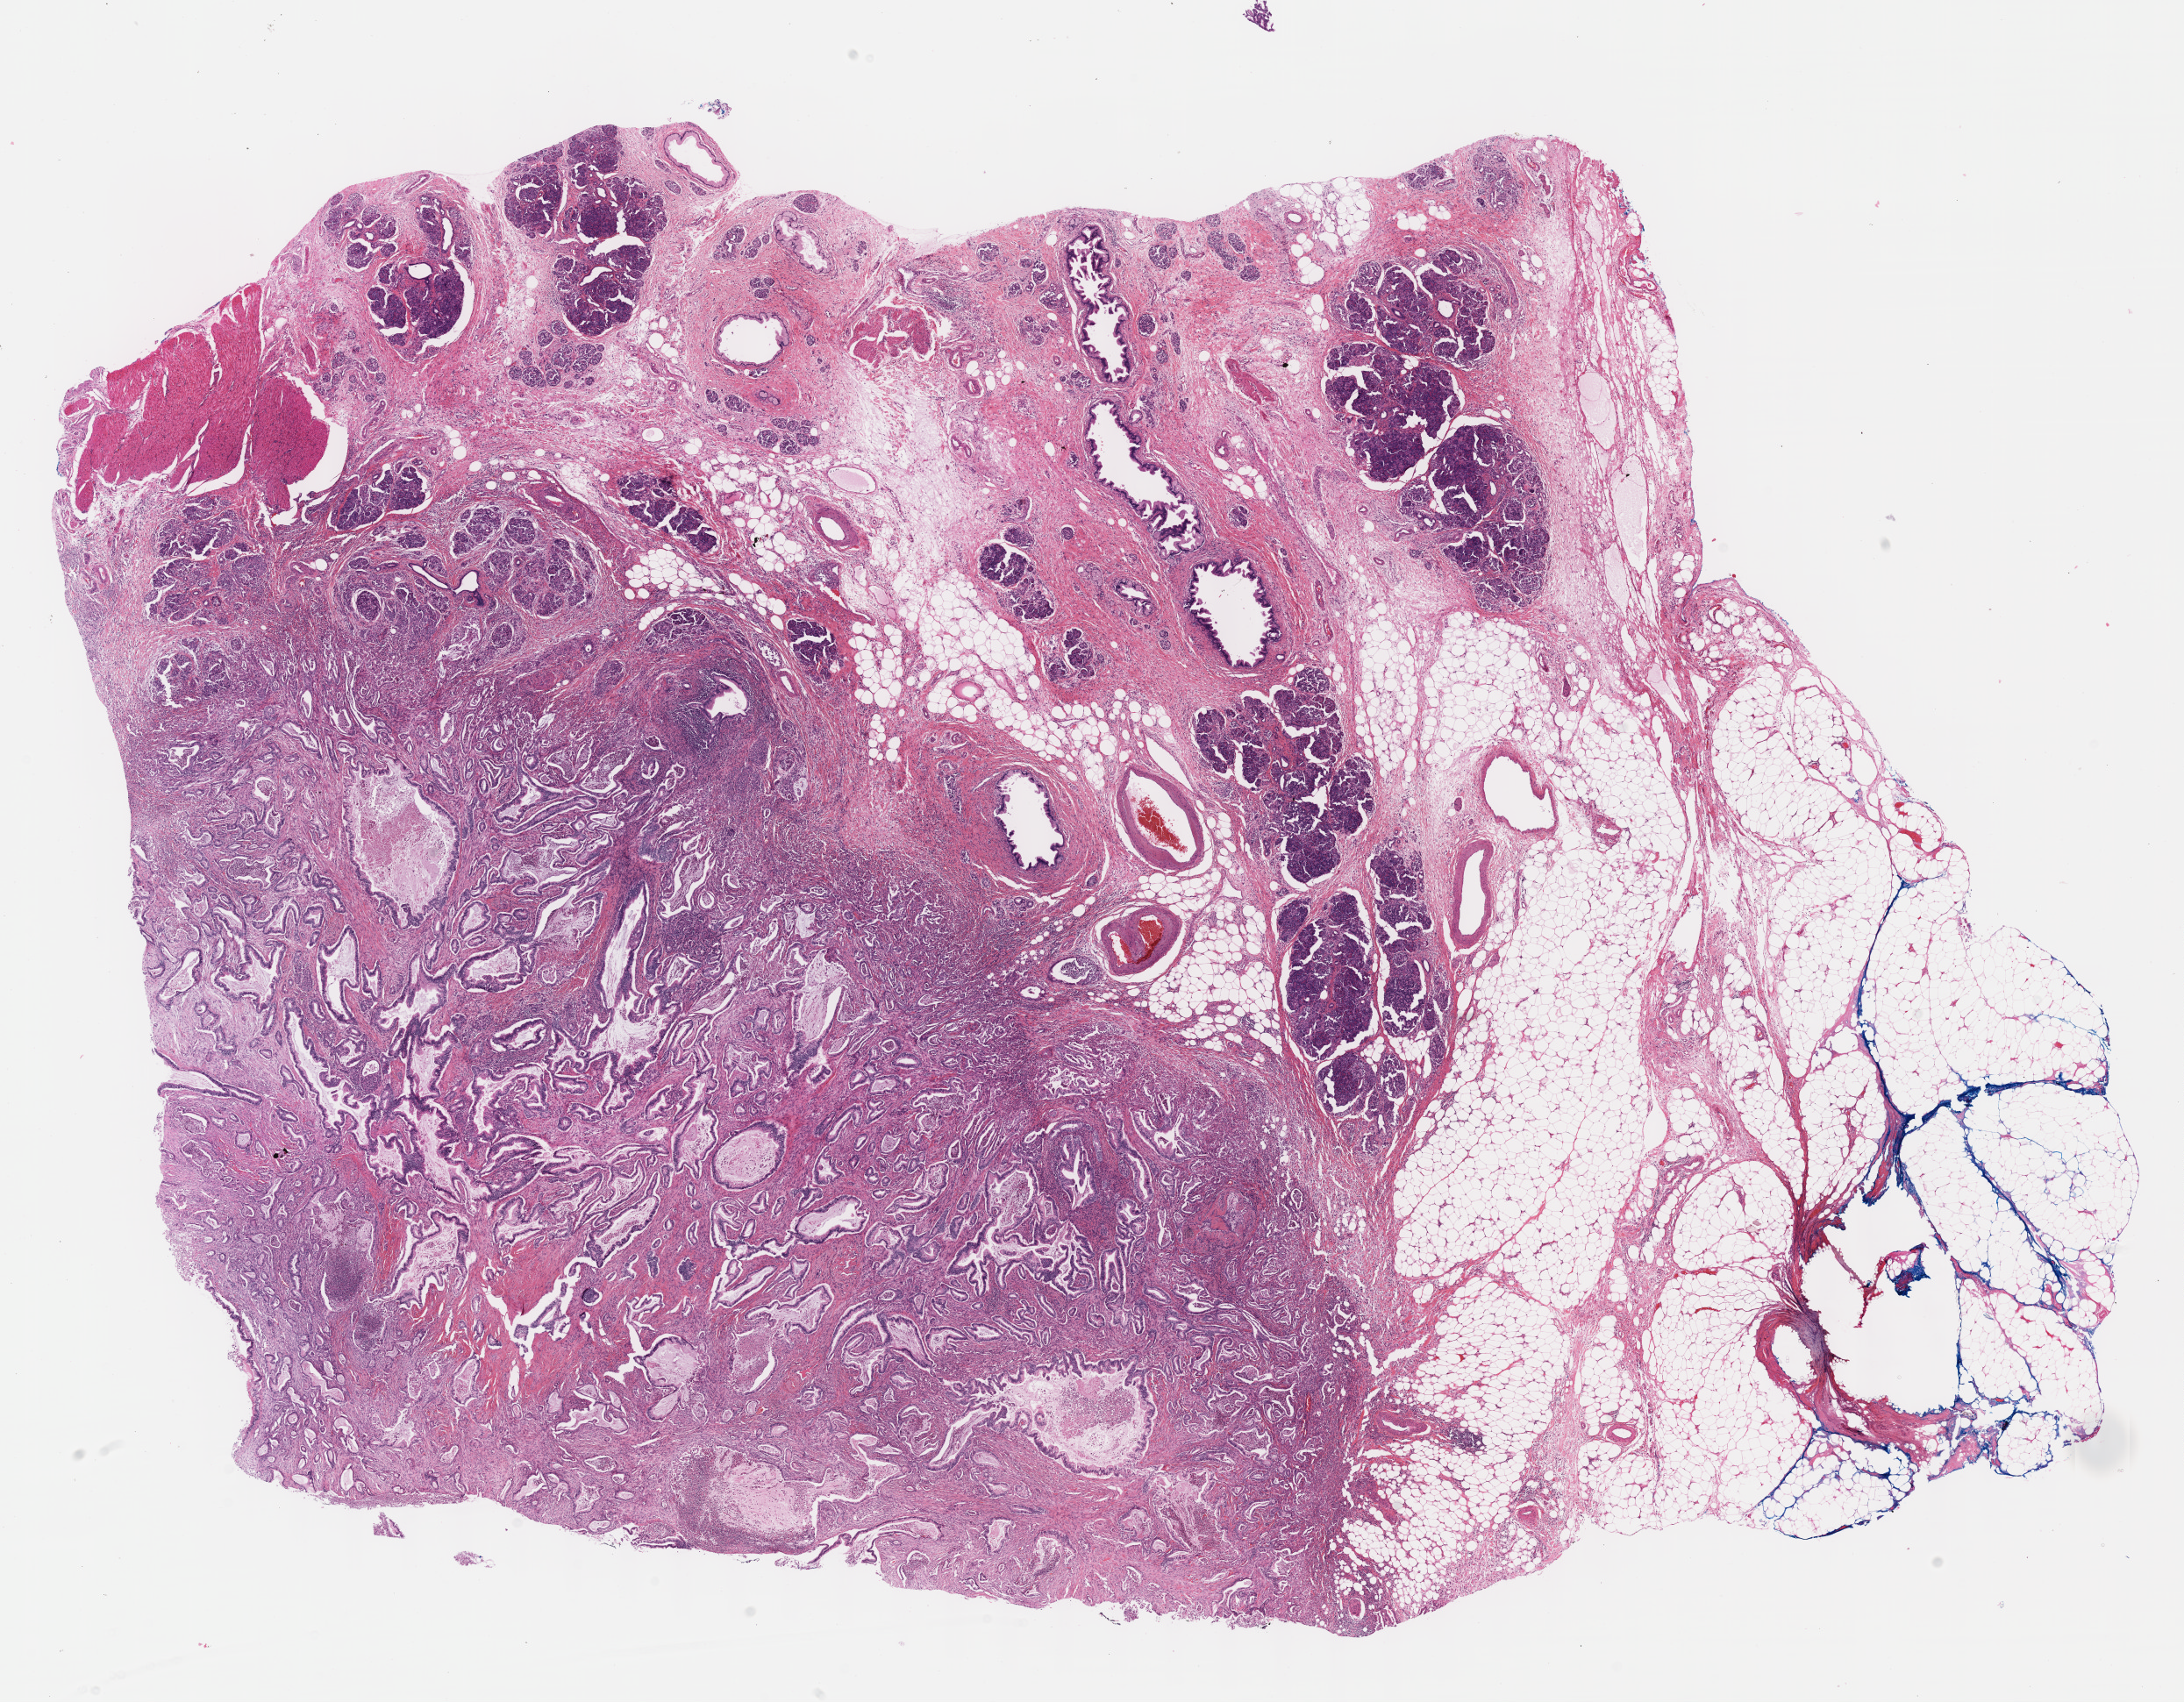
Digitized Hematoxylin and eosin (H&E) stained tissue section (whole slide), shown as a low-resolution overview of the whole scanned area (about 20.1 x 15.7 mm). FFPE section. Sample: primary tumour, pancreas. Female, age 74 years at initial diagnosis. Histologic grade: G1 (well differentiated).
AJCC pathologic stage: IIA (7th edition). Pathologic diagnosis: Infiltrating duct carcinoma, NOS. TNM: T3 N0 M0.